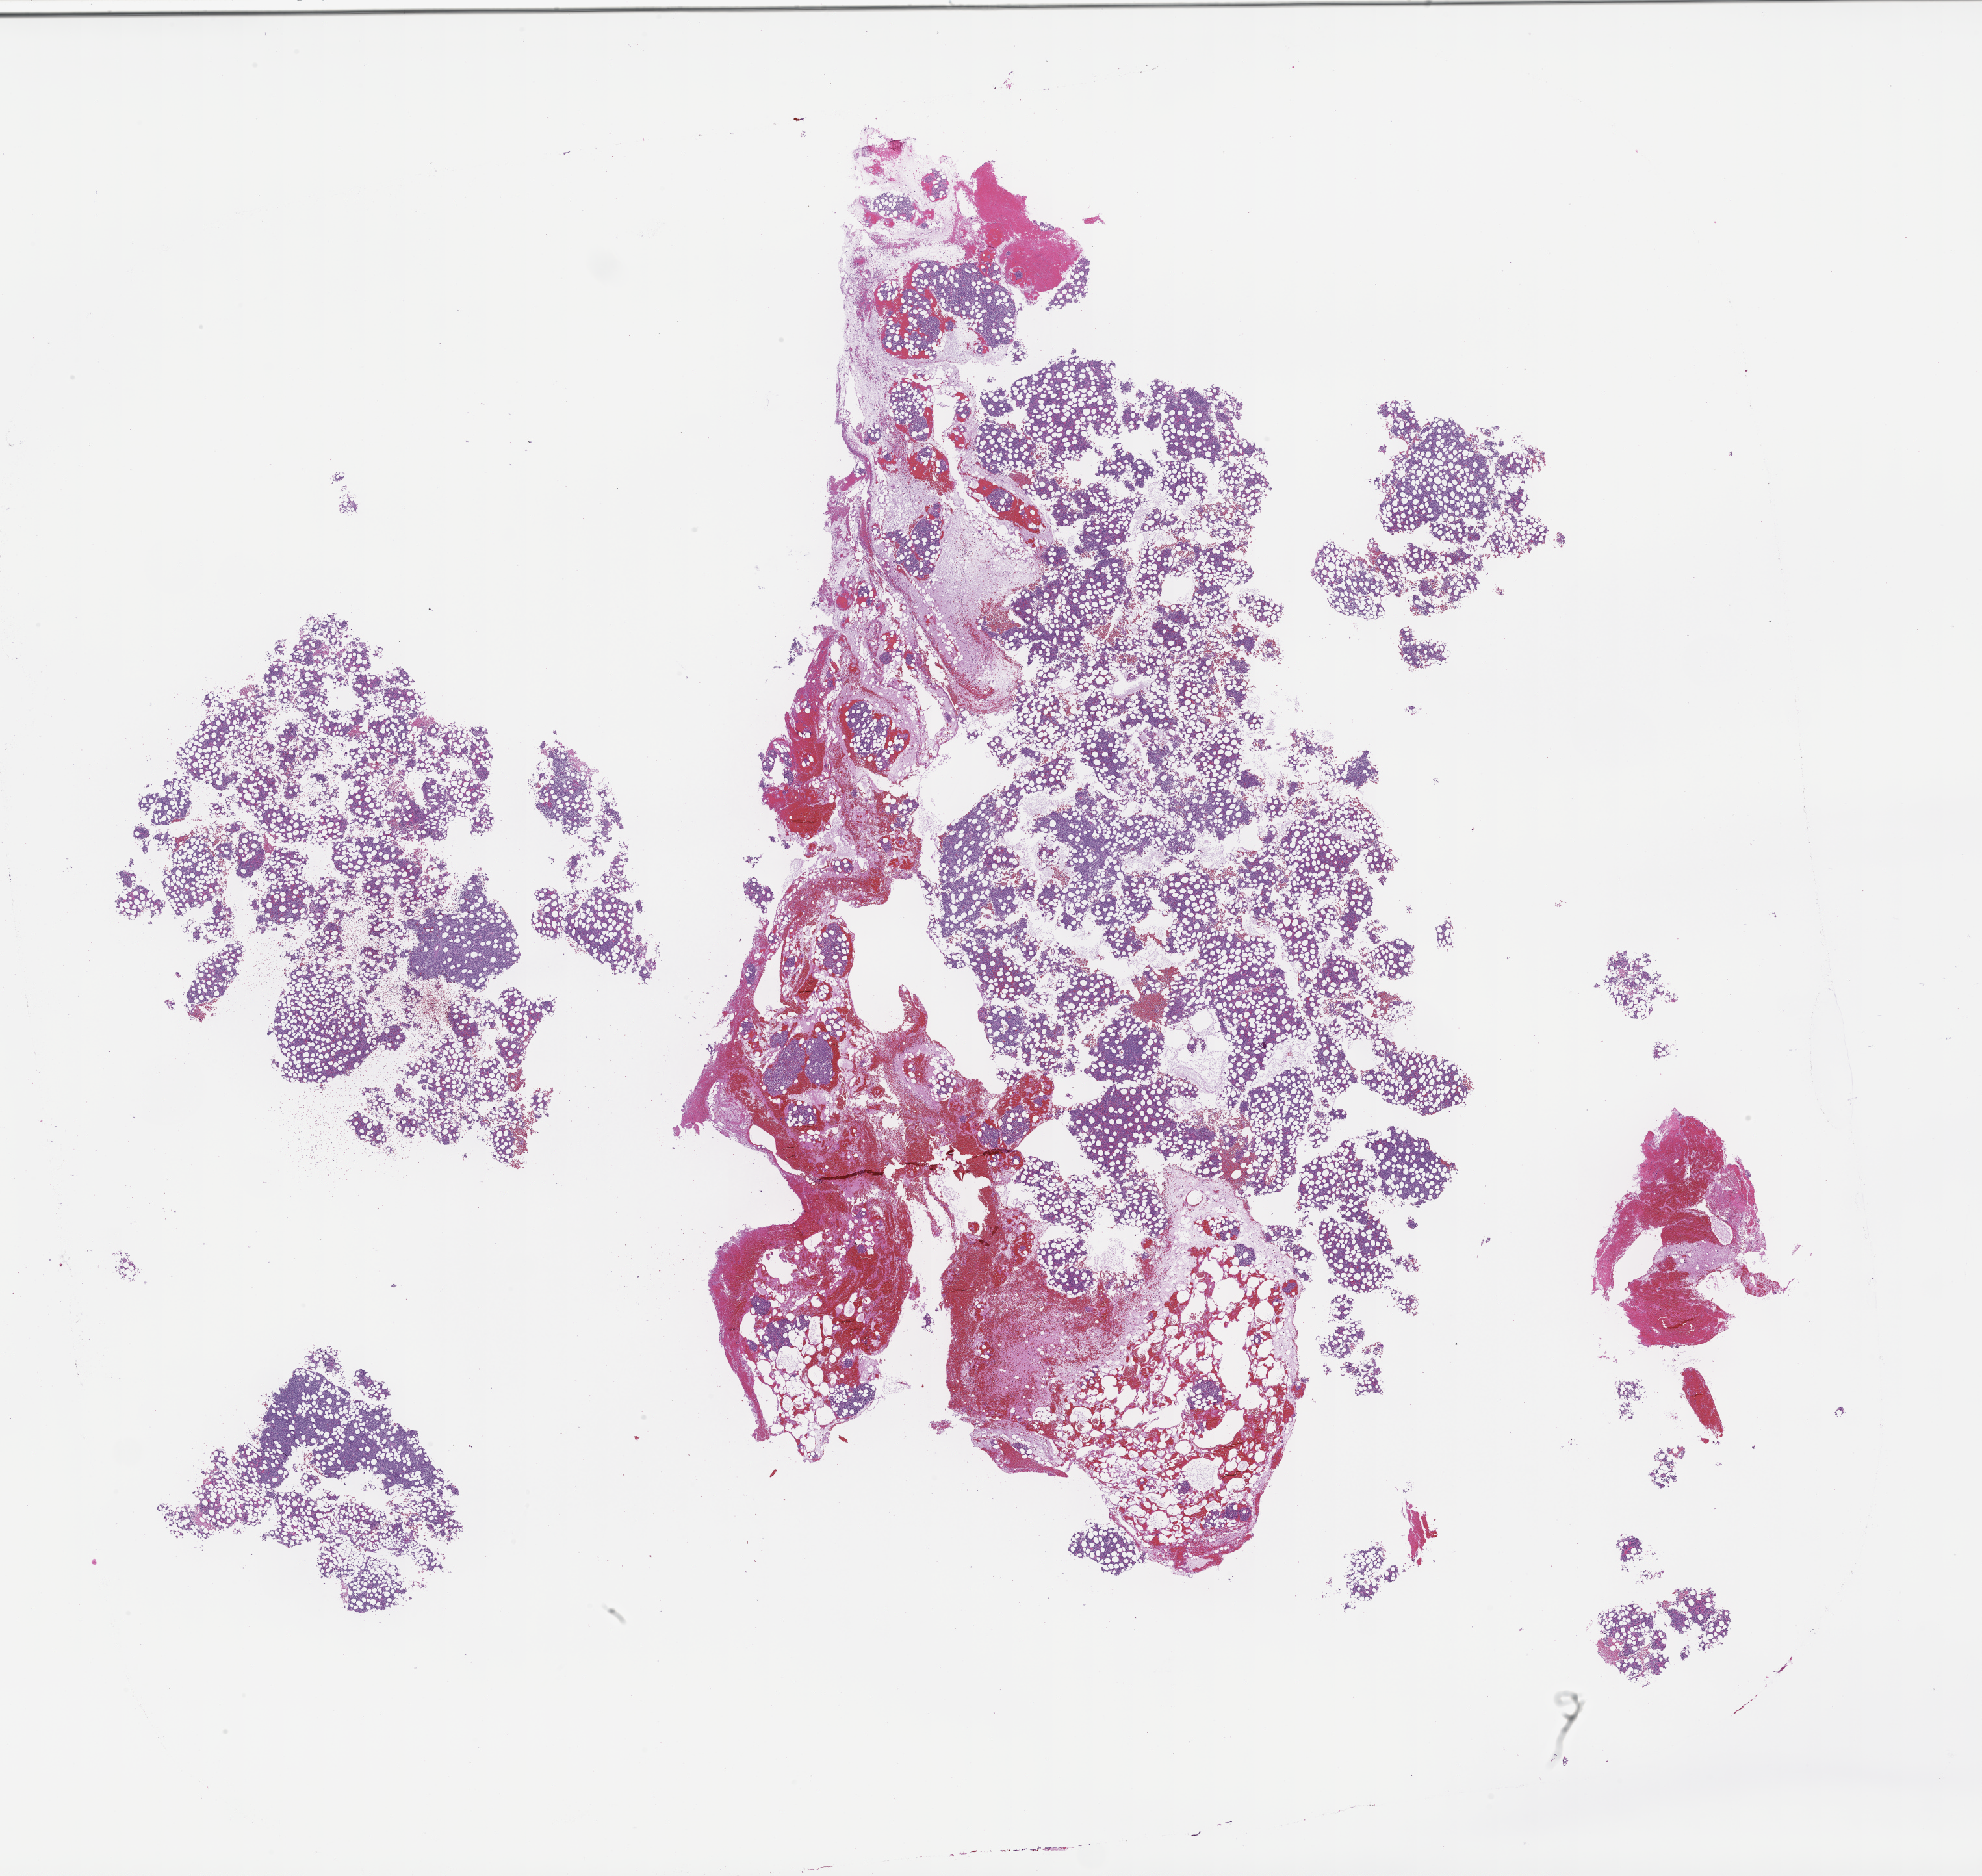
Whole-slide image, H&E stain, low-resolution overview of the scanned area, about 24.6 x 23.3 mm. FFPE section. Tissue site: bone marrow. Archival tissue. Male patient.
This section: primary tumor. Diagnosis: Plasma Cell Myeloma.